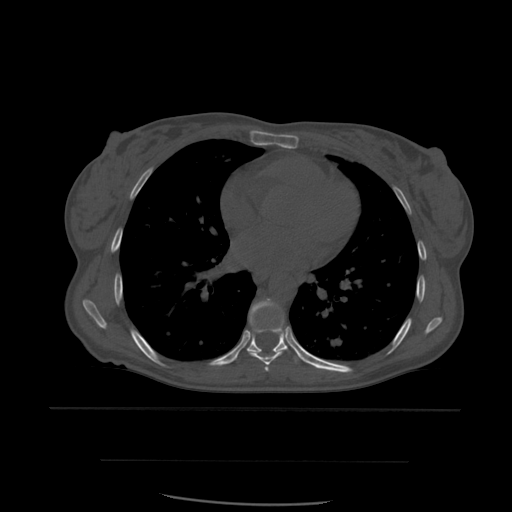
CT including the spine, one axial slice; slice 366 of 574 in the series (ordered by position); bone window (W 1800 / L 400 HU); 1.25 mm slice thickness; 512 × 512 image matrix. Patient age 48 years. From the clinical record (not read from this slice): primary cancer: lung.
Annotated regions visible in this slice (semi-automatic segmentation, software-assisted and operator-edited):
- T6 vertebra: box from (x=265, y=368) to (x=268, y=371) px
- T7 vertebra: (x=247, y=299)–(x=285, y=372)
- T8 vertebra: (x=235, y=326)–(x=297, y=363)